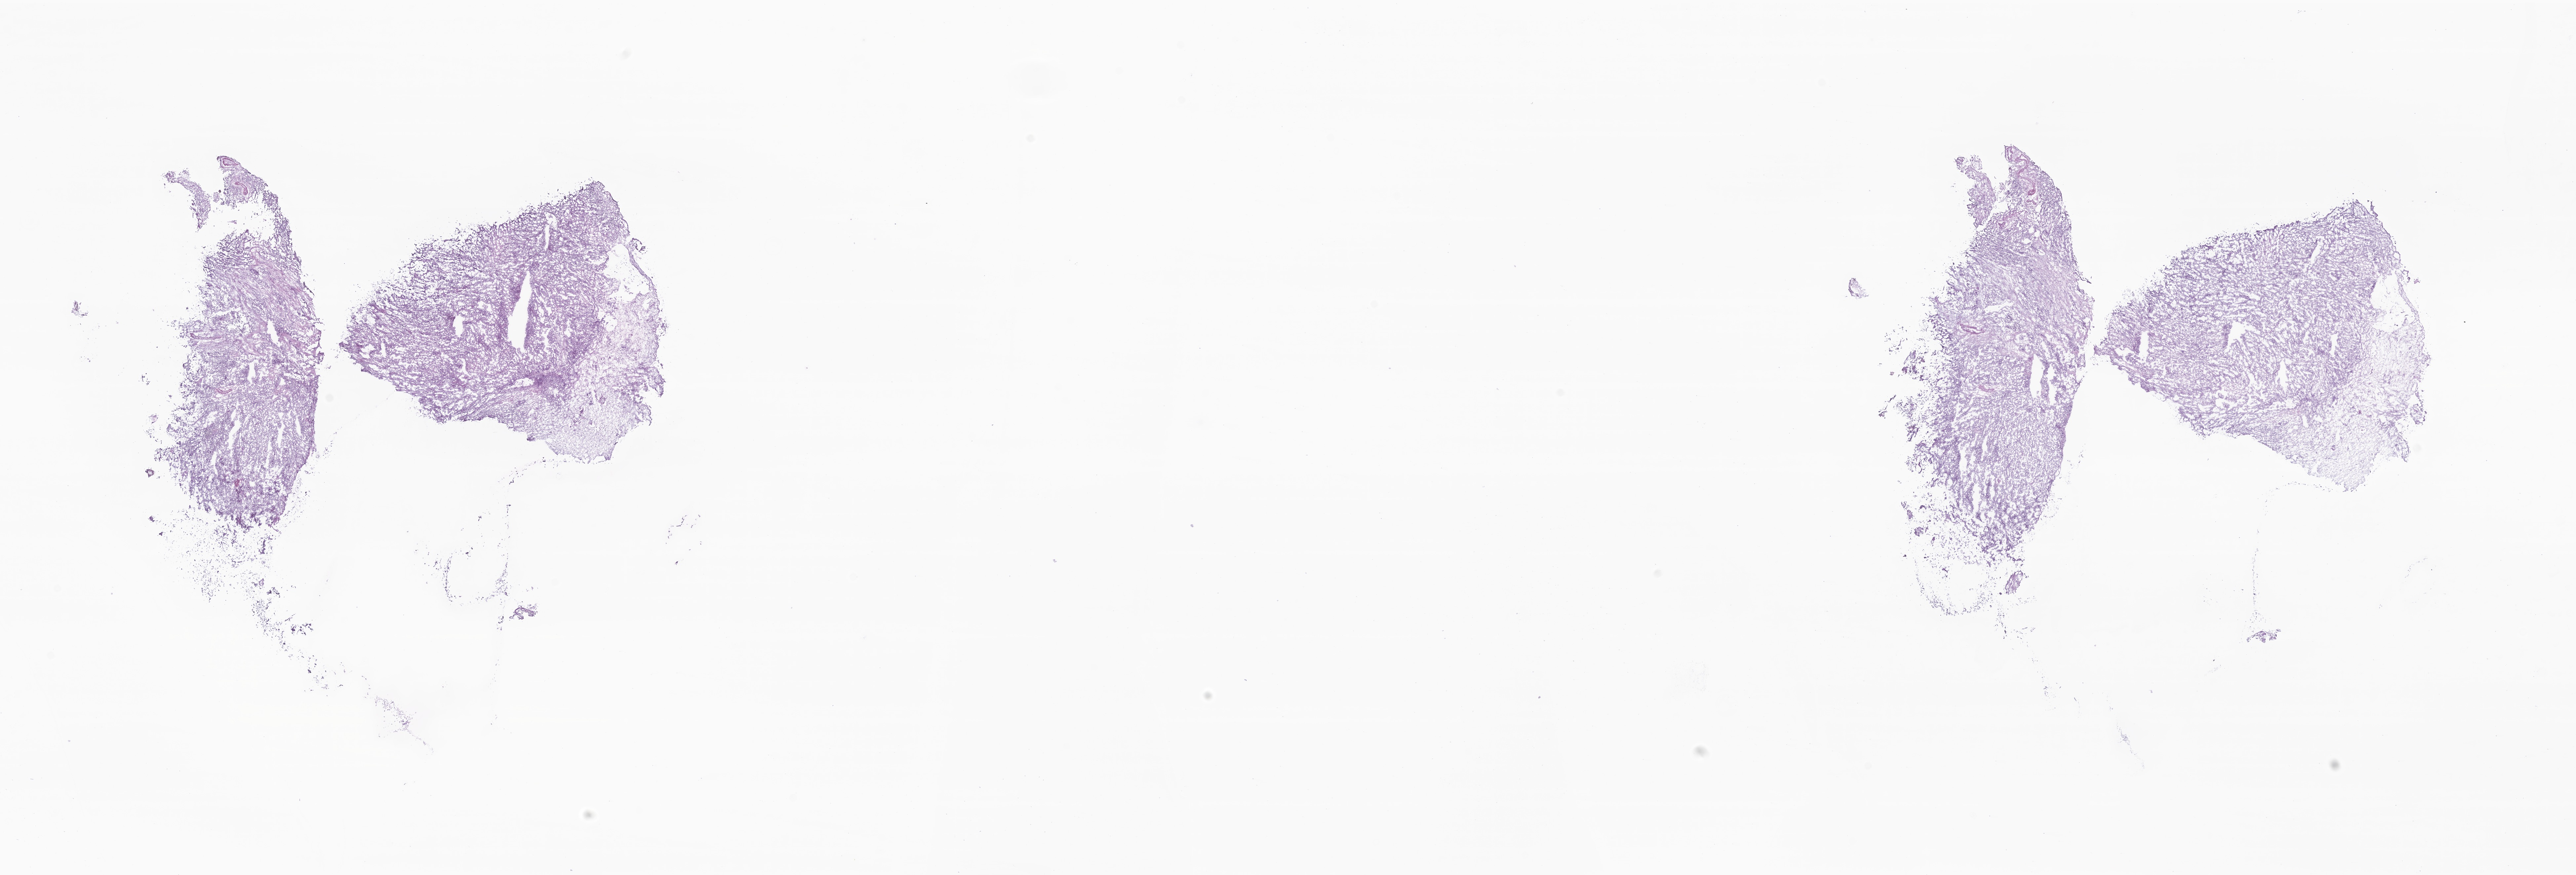
Digitized haematoxylin and eosin-stained section of tumor tissue from the brain, a low-resolution overview of the entire scanned area, about 32.9 x 11.2 mm; frozen section. Patient: male, age 213 months (17 years 9 months).
Recorded diagnosis: Mixed germ cell tumor.